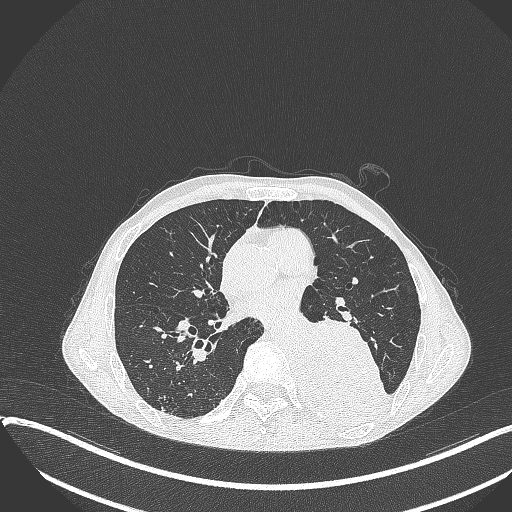
Chest CT, one axial slice. 120 kVp. Lung window (W 1500 / L -600 HU). 1 mm slice thickness. 512 × 512 image matrix, field of view 400 × 400 mm. Patient: male, 57 years. From the clinical record (not read from this slice): clinical TNM (as recorded): T4 N0 M0.
Outlined on this slice (bounding box drawn by a radiologist):
- lung tumour (recorded histology: squamous cell carcinoma): bounding box (x1, y1, x2, y2) in pixels: (299, 311, 390, 425)